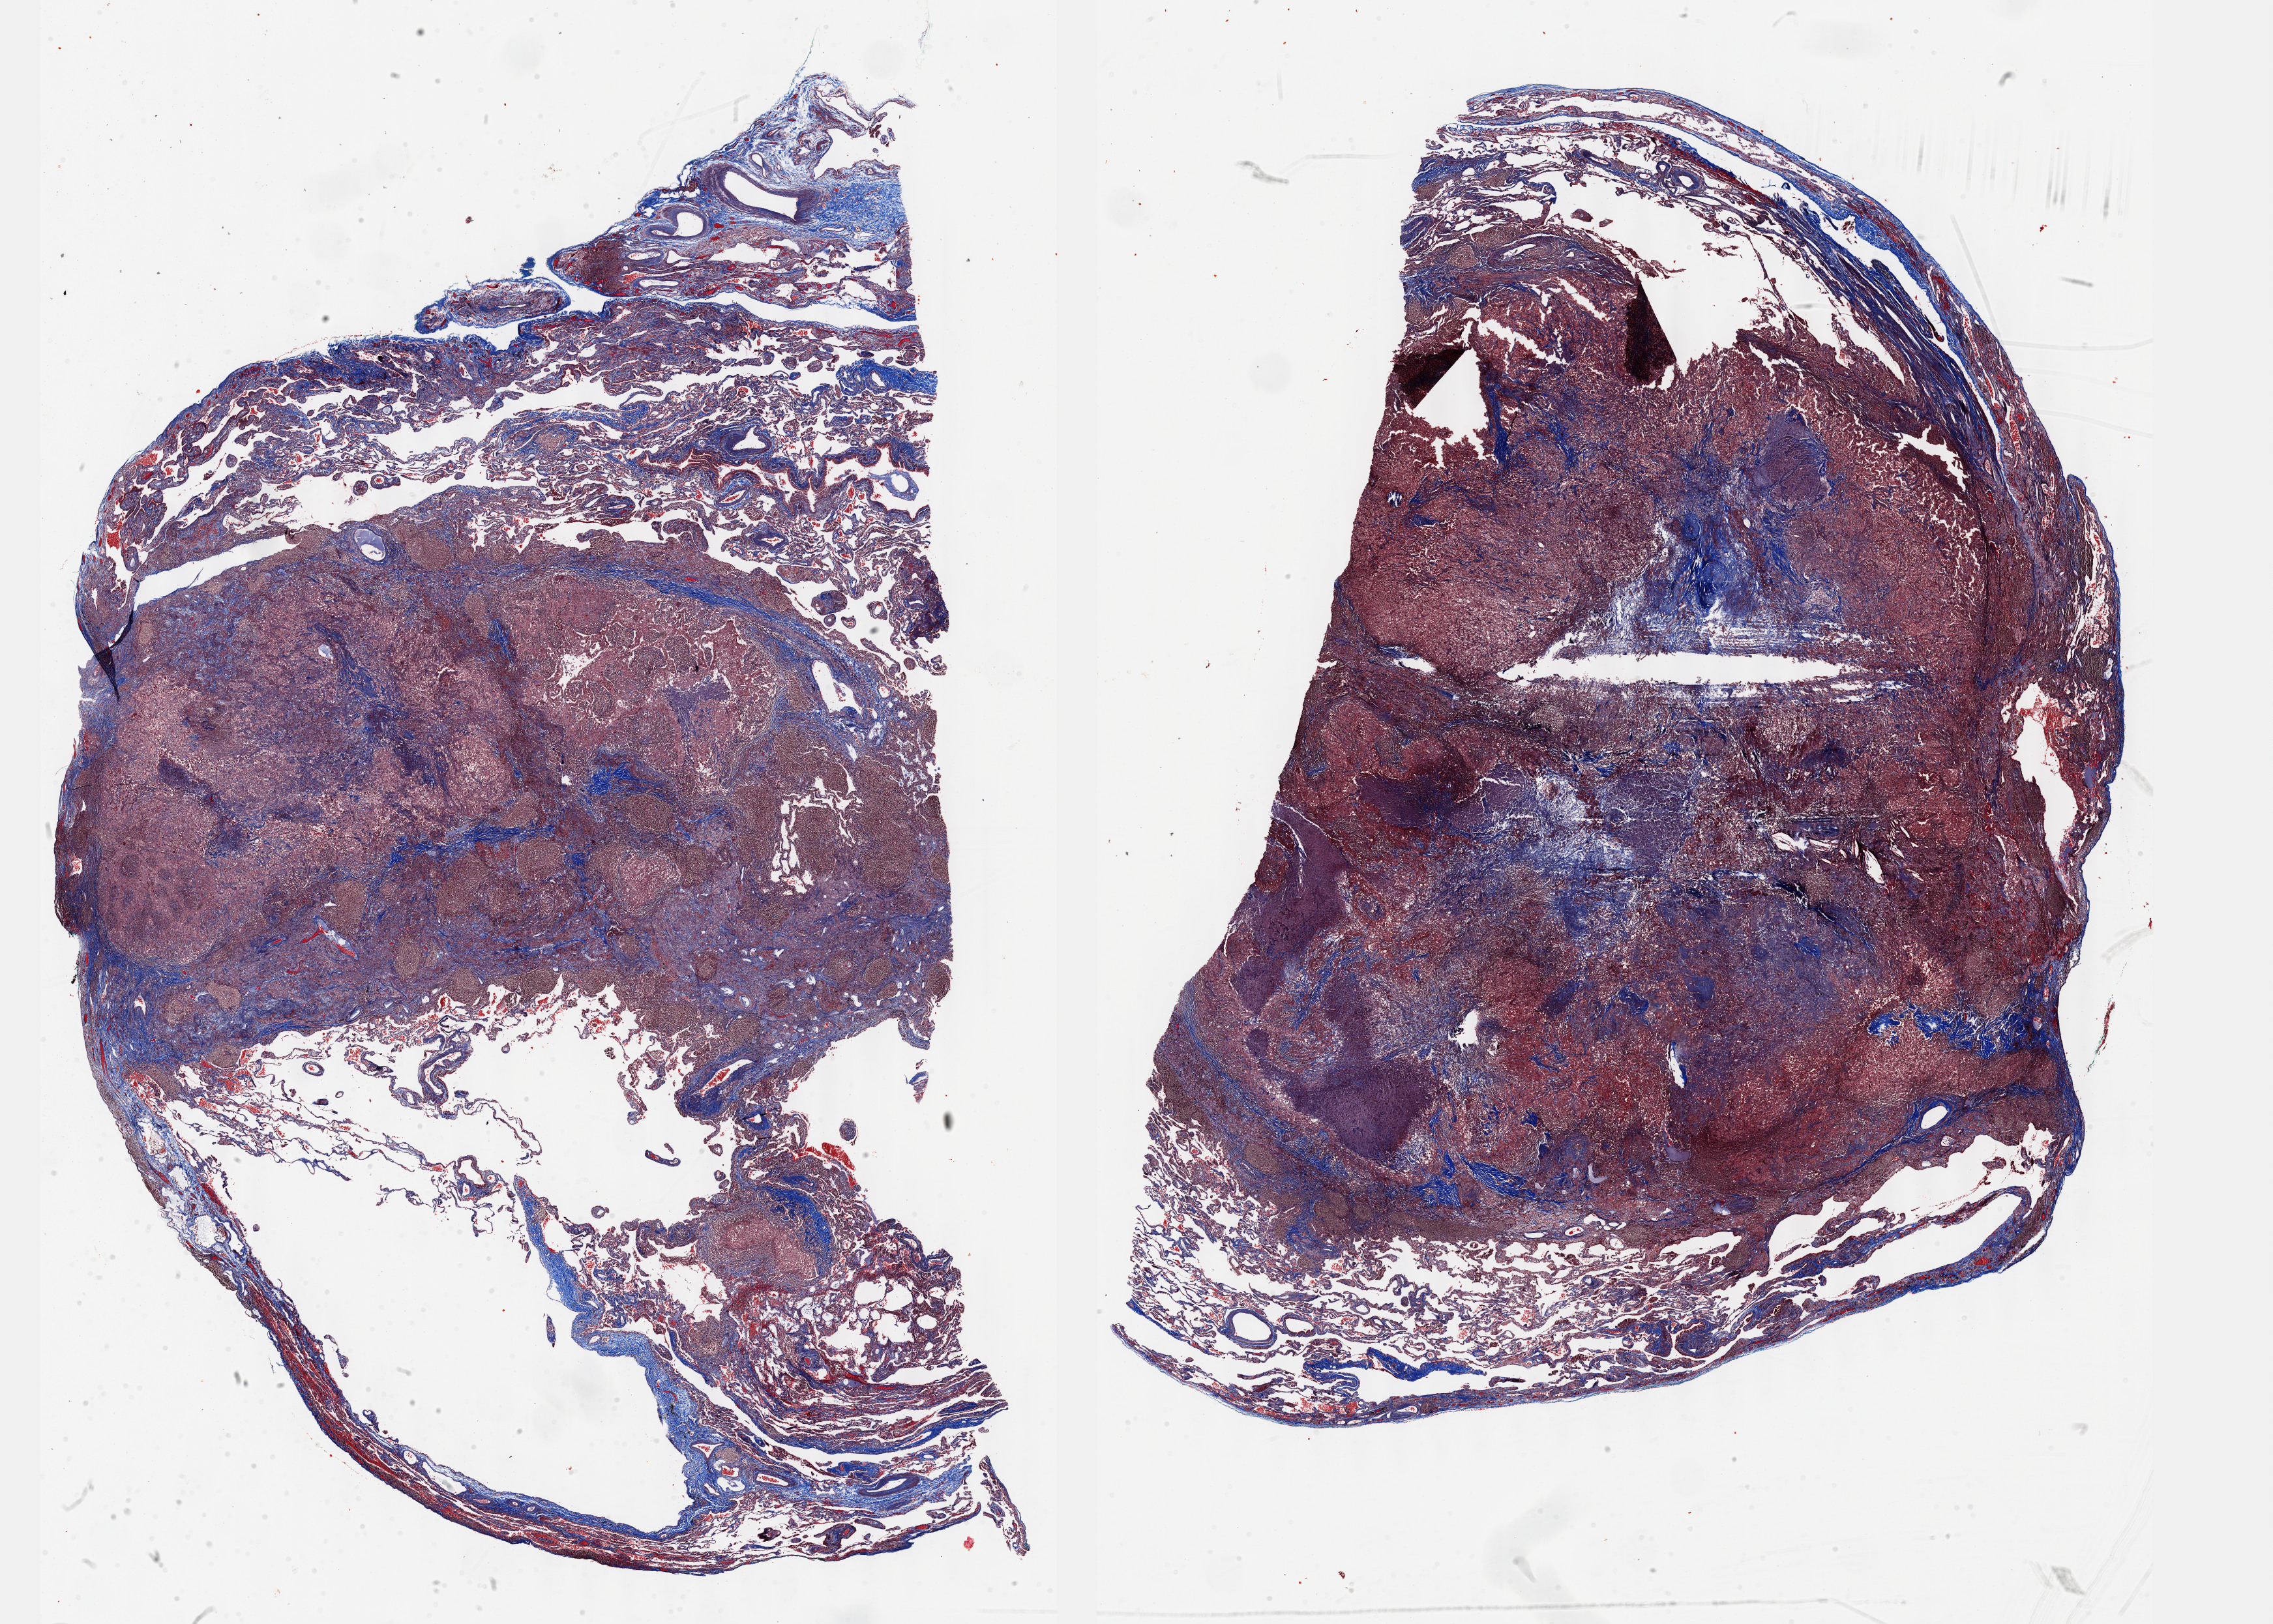
Digitized Hematoxylin and eosin (H&E) stained tissue section (whole slide), low-resolution overview of the scanned area, about 28.2 x 20.1 mm. Formalin-fixed paraffin-embedded (FFPE) diagnostic section. Primary tumour sample from the lung. Female patient; age at initial diagnosis 72 years.
AJCC pathologic stage: IB (6th edition). Histologic diagnosis: Adenocarcinoma, NOS. Laterality: right.